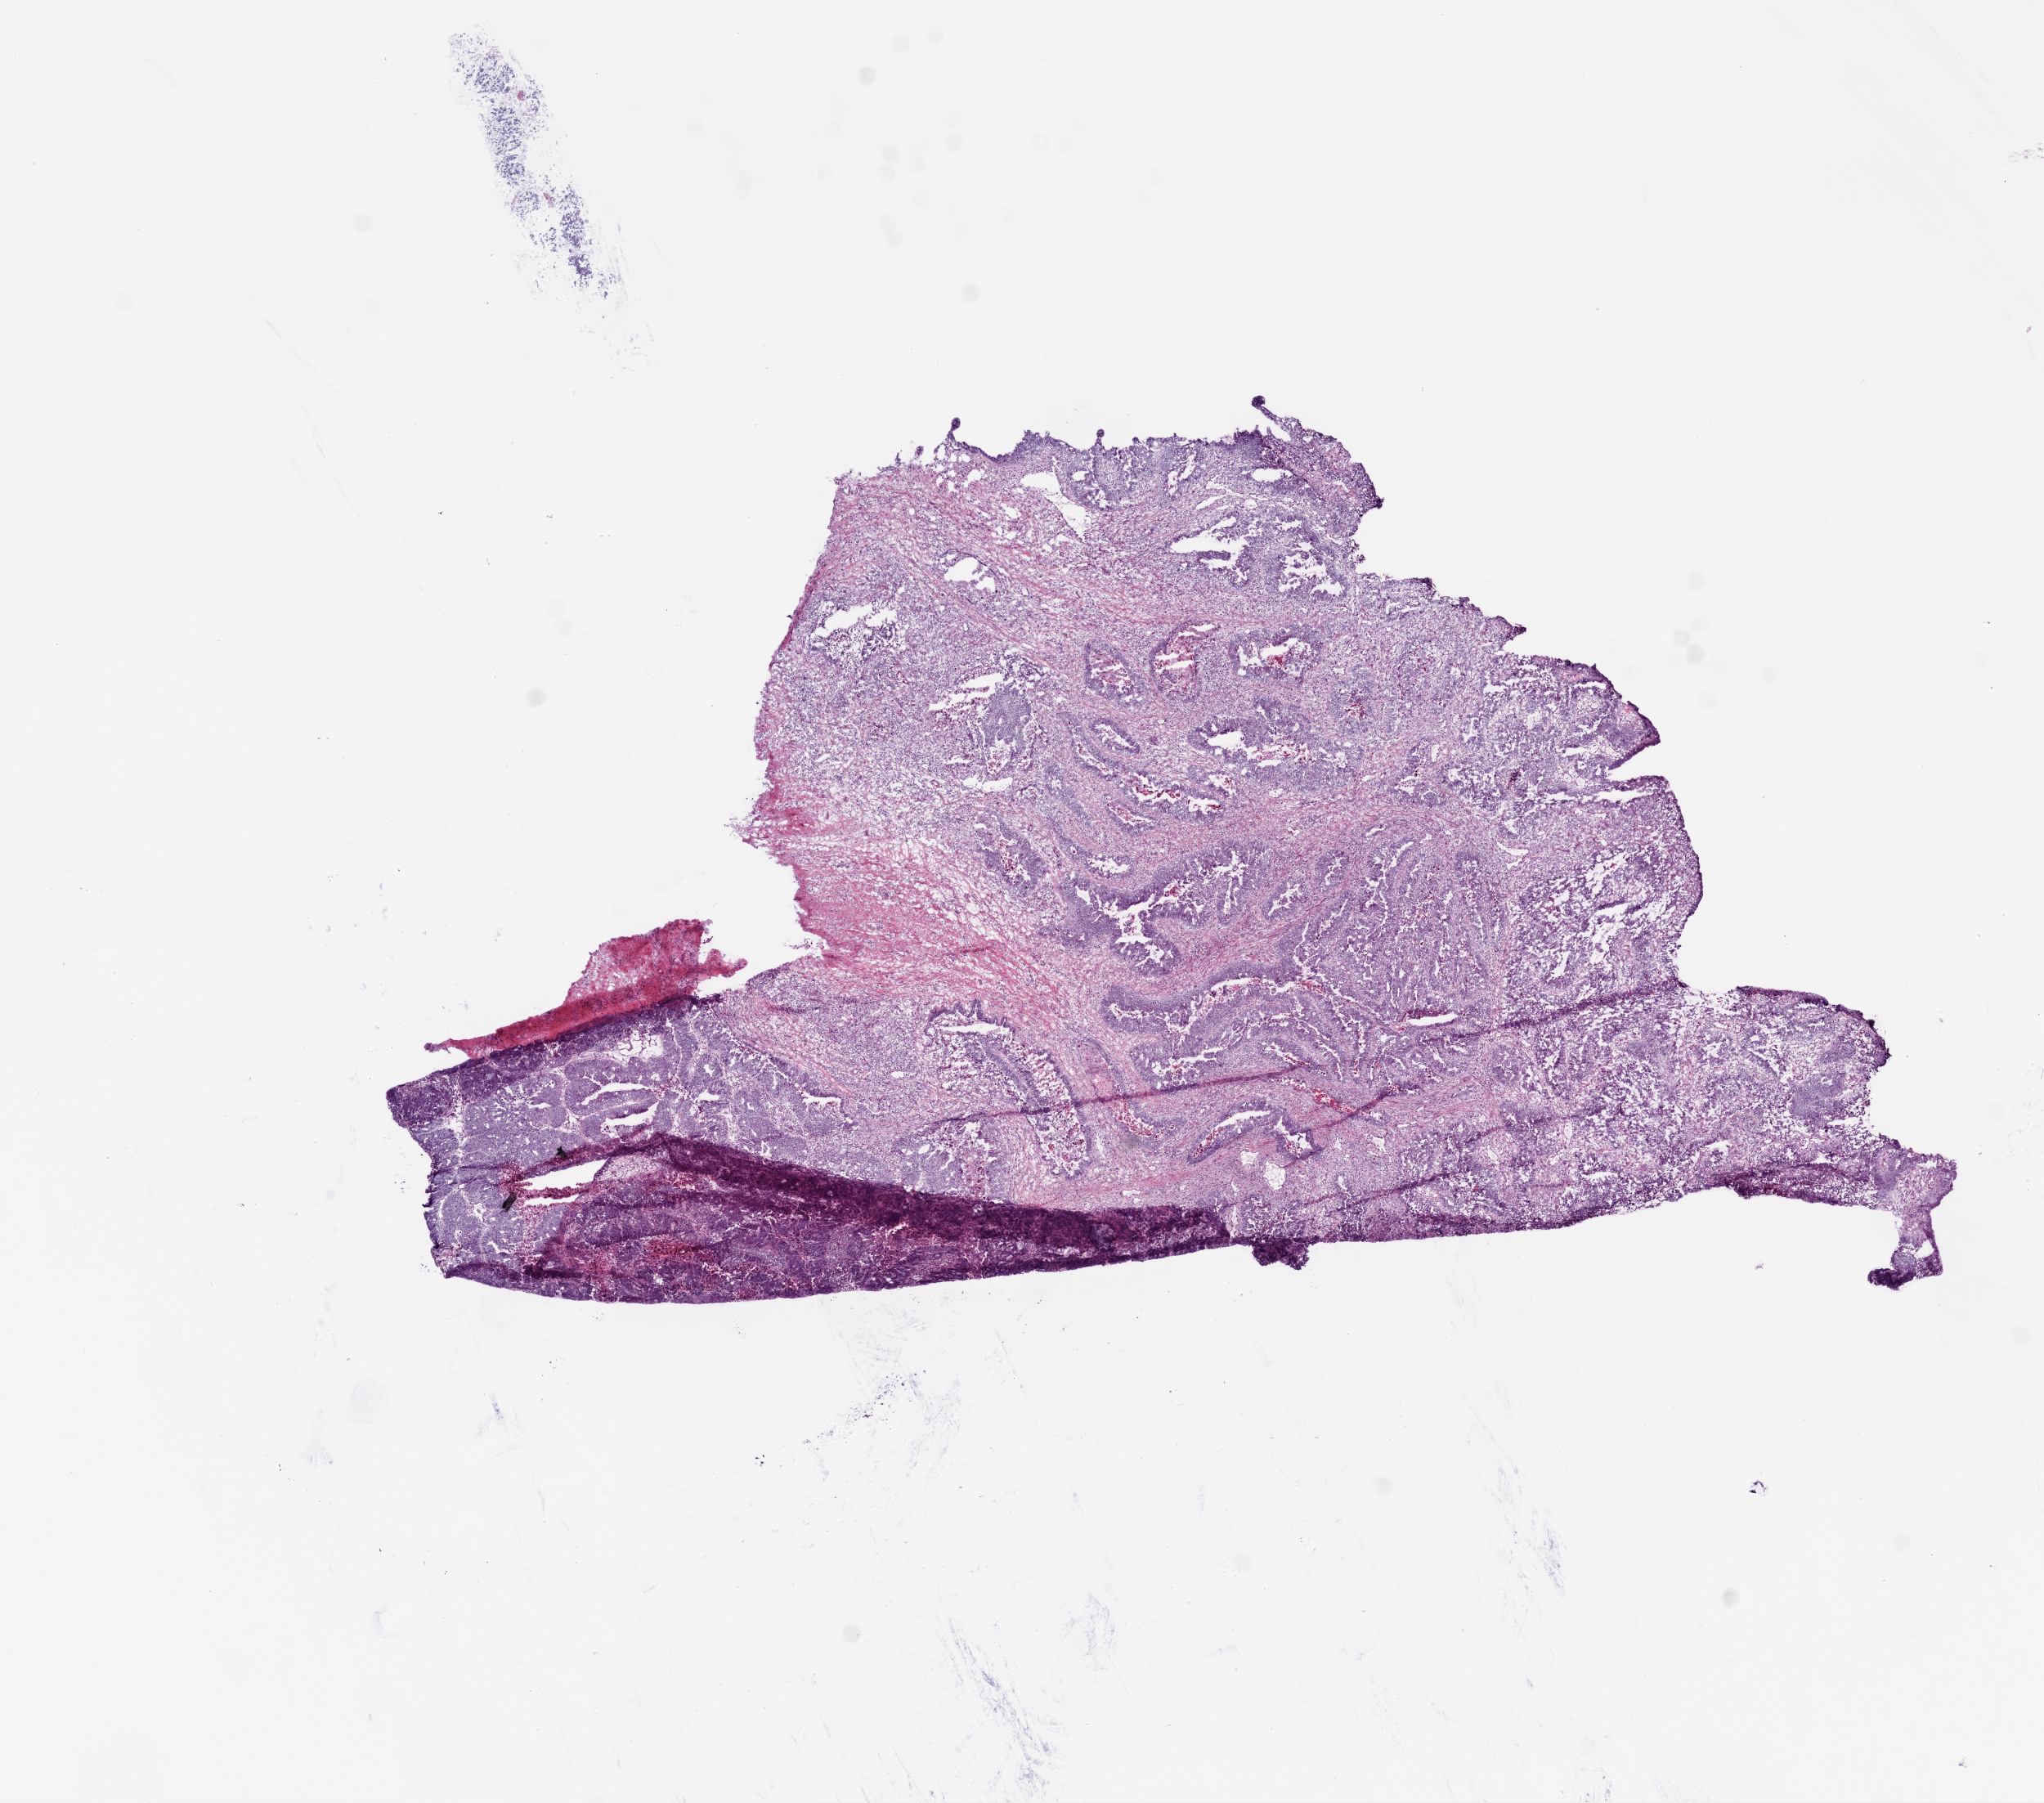
Digitized Hematoxylin and eosin (H&E) stained tissue section (whole slide), shown as a low-resolution overview of the whole scanned area (about 10.0 x 8.8 mm); frozen section from the top of the tissue portion; rectum, primary tumour sample. Male, age 61 years at initial diagnosis. Pathologist review of this section (percent, as recorded): tumour cells 60%, tumour nuclei 75%, normal cells 0%, stromal cells 30%, necrosis 10%.
* AJCC pathologic stage: IIA
* pathologic diagnosis: Adenocarcinoma, NOS
* TNM: T3 N0 M0